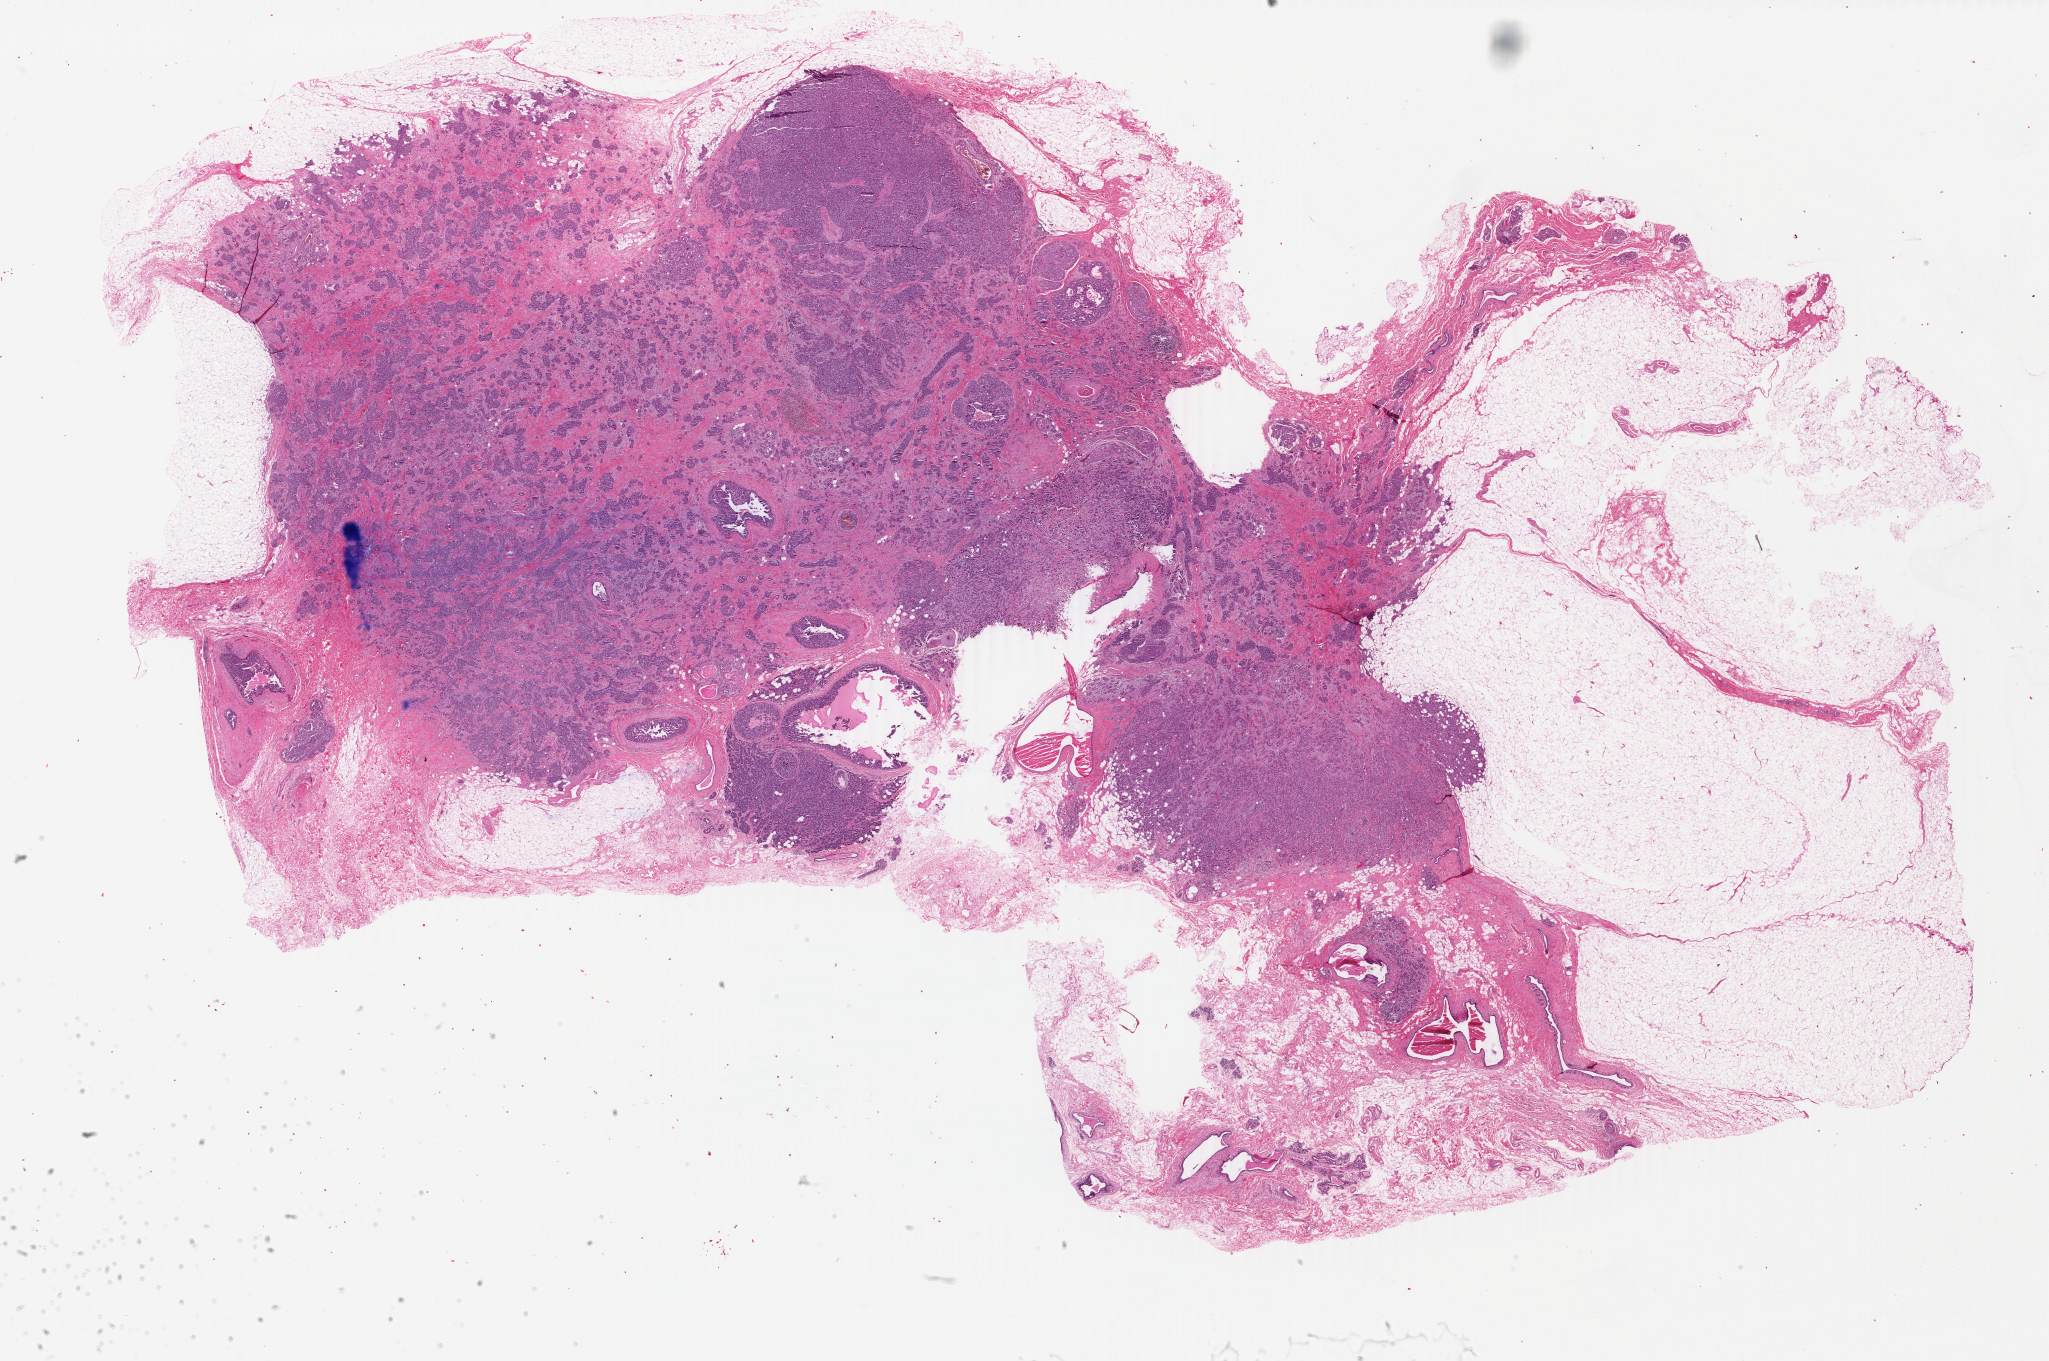
Whole-slide histology image, Hematoxylin and eosin (H&E) stained — a low-resolution overview of the entire scanned area, about 32.6 x 21.7 mm (acquisition: 40x scan), formalin-fixed paraffin-embedded (FFPE) diagnostic section, breast, primary tumour sample. Female, age 60 years at initial diagnosis.
AJCC pathologic stage: IIA. Lymph nodes positive (case pathology): 0 of 16 examined. Laterality: left. Histologic diagnosis: Infiltrating duct carcinoma, NOS. TNM: T2 N0 (i-) M0.